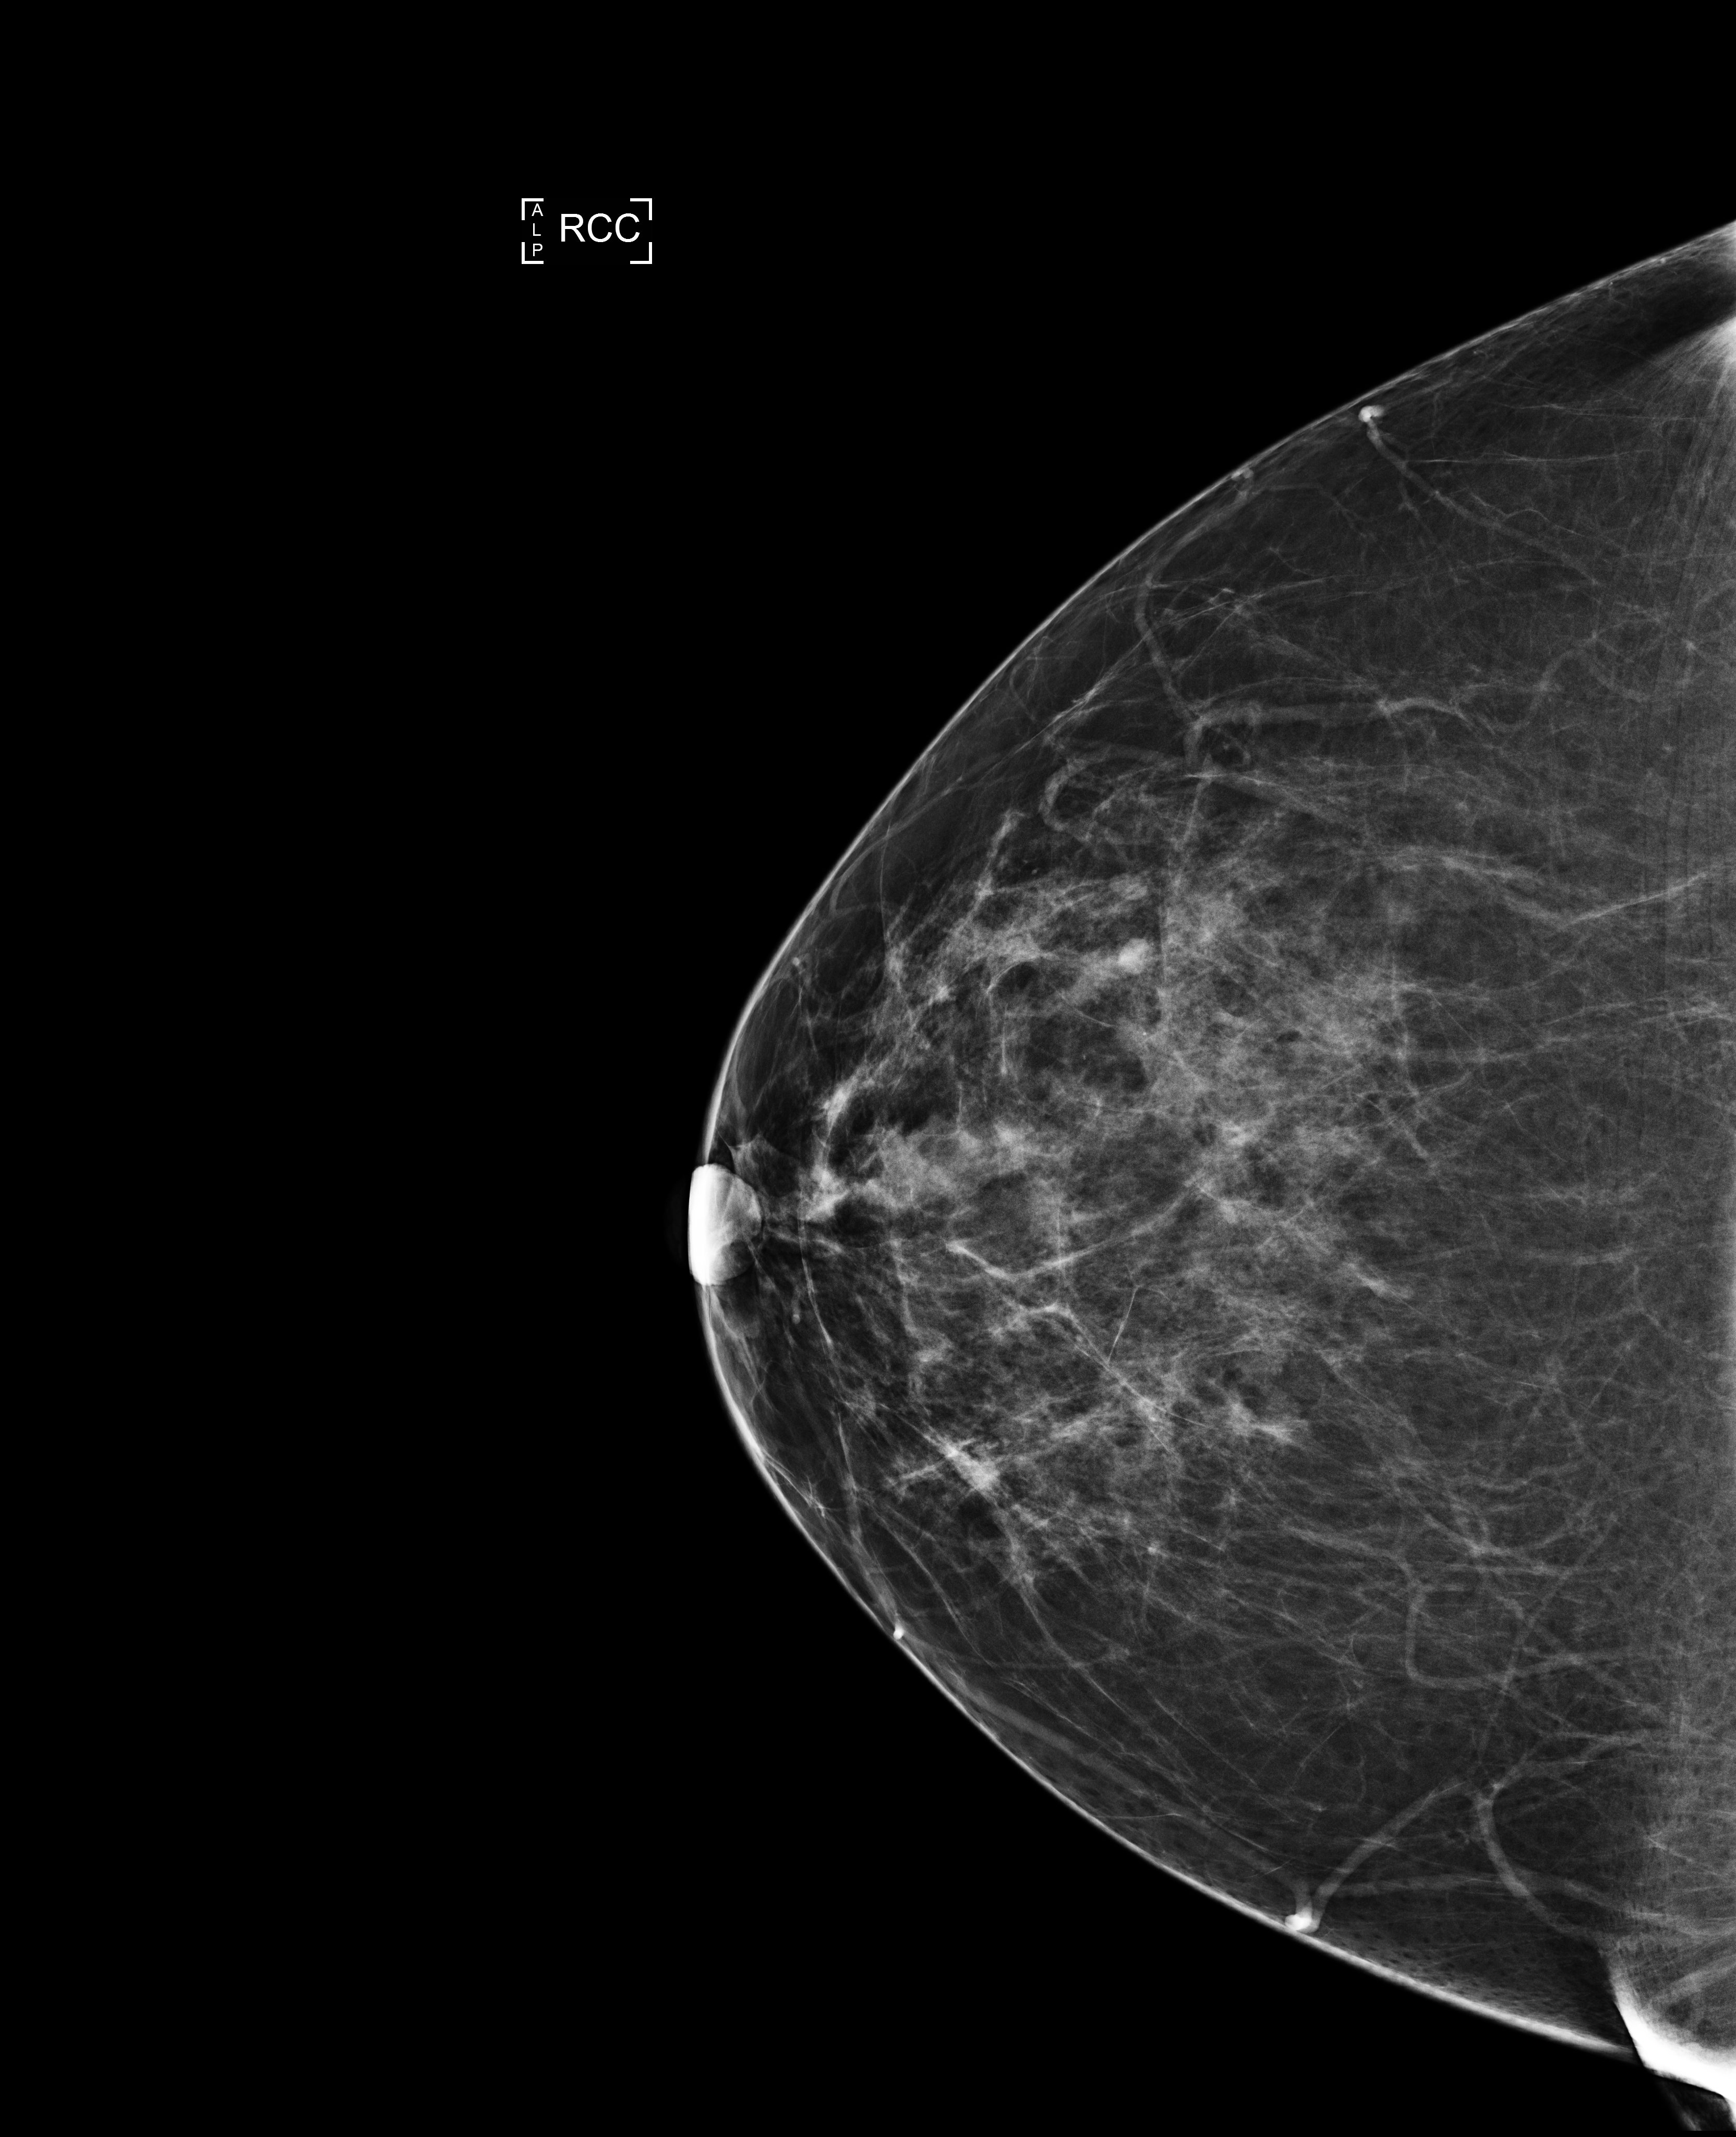
Annual screening mammography examination. Female patient, age 52 years.
Image type: full-field digital mammogram. Breast: right. Projection: craniocaudal (CC) view. Breast density at the screening exam (both breasts): heterogeneously dense (BI-RADS density category c). Final BI-RADS category for the screening round (tomosynthesis exam, both breasts): category 1. Recall: no recall after this screen.